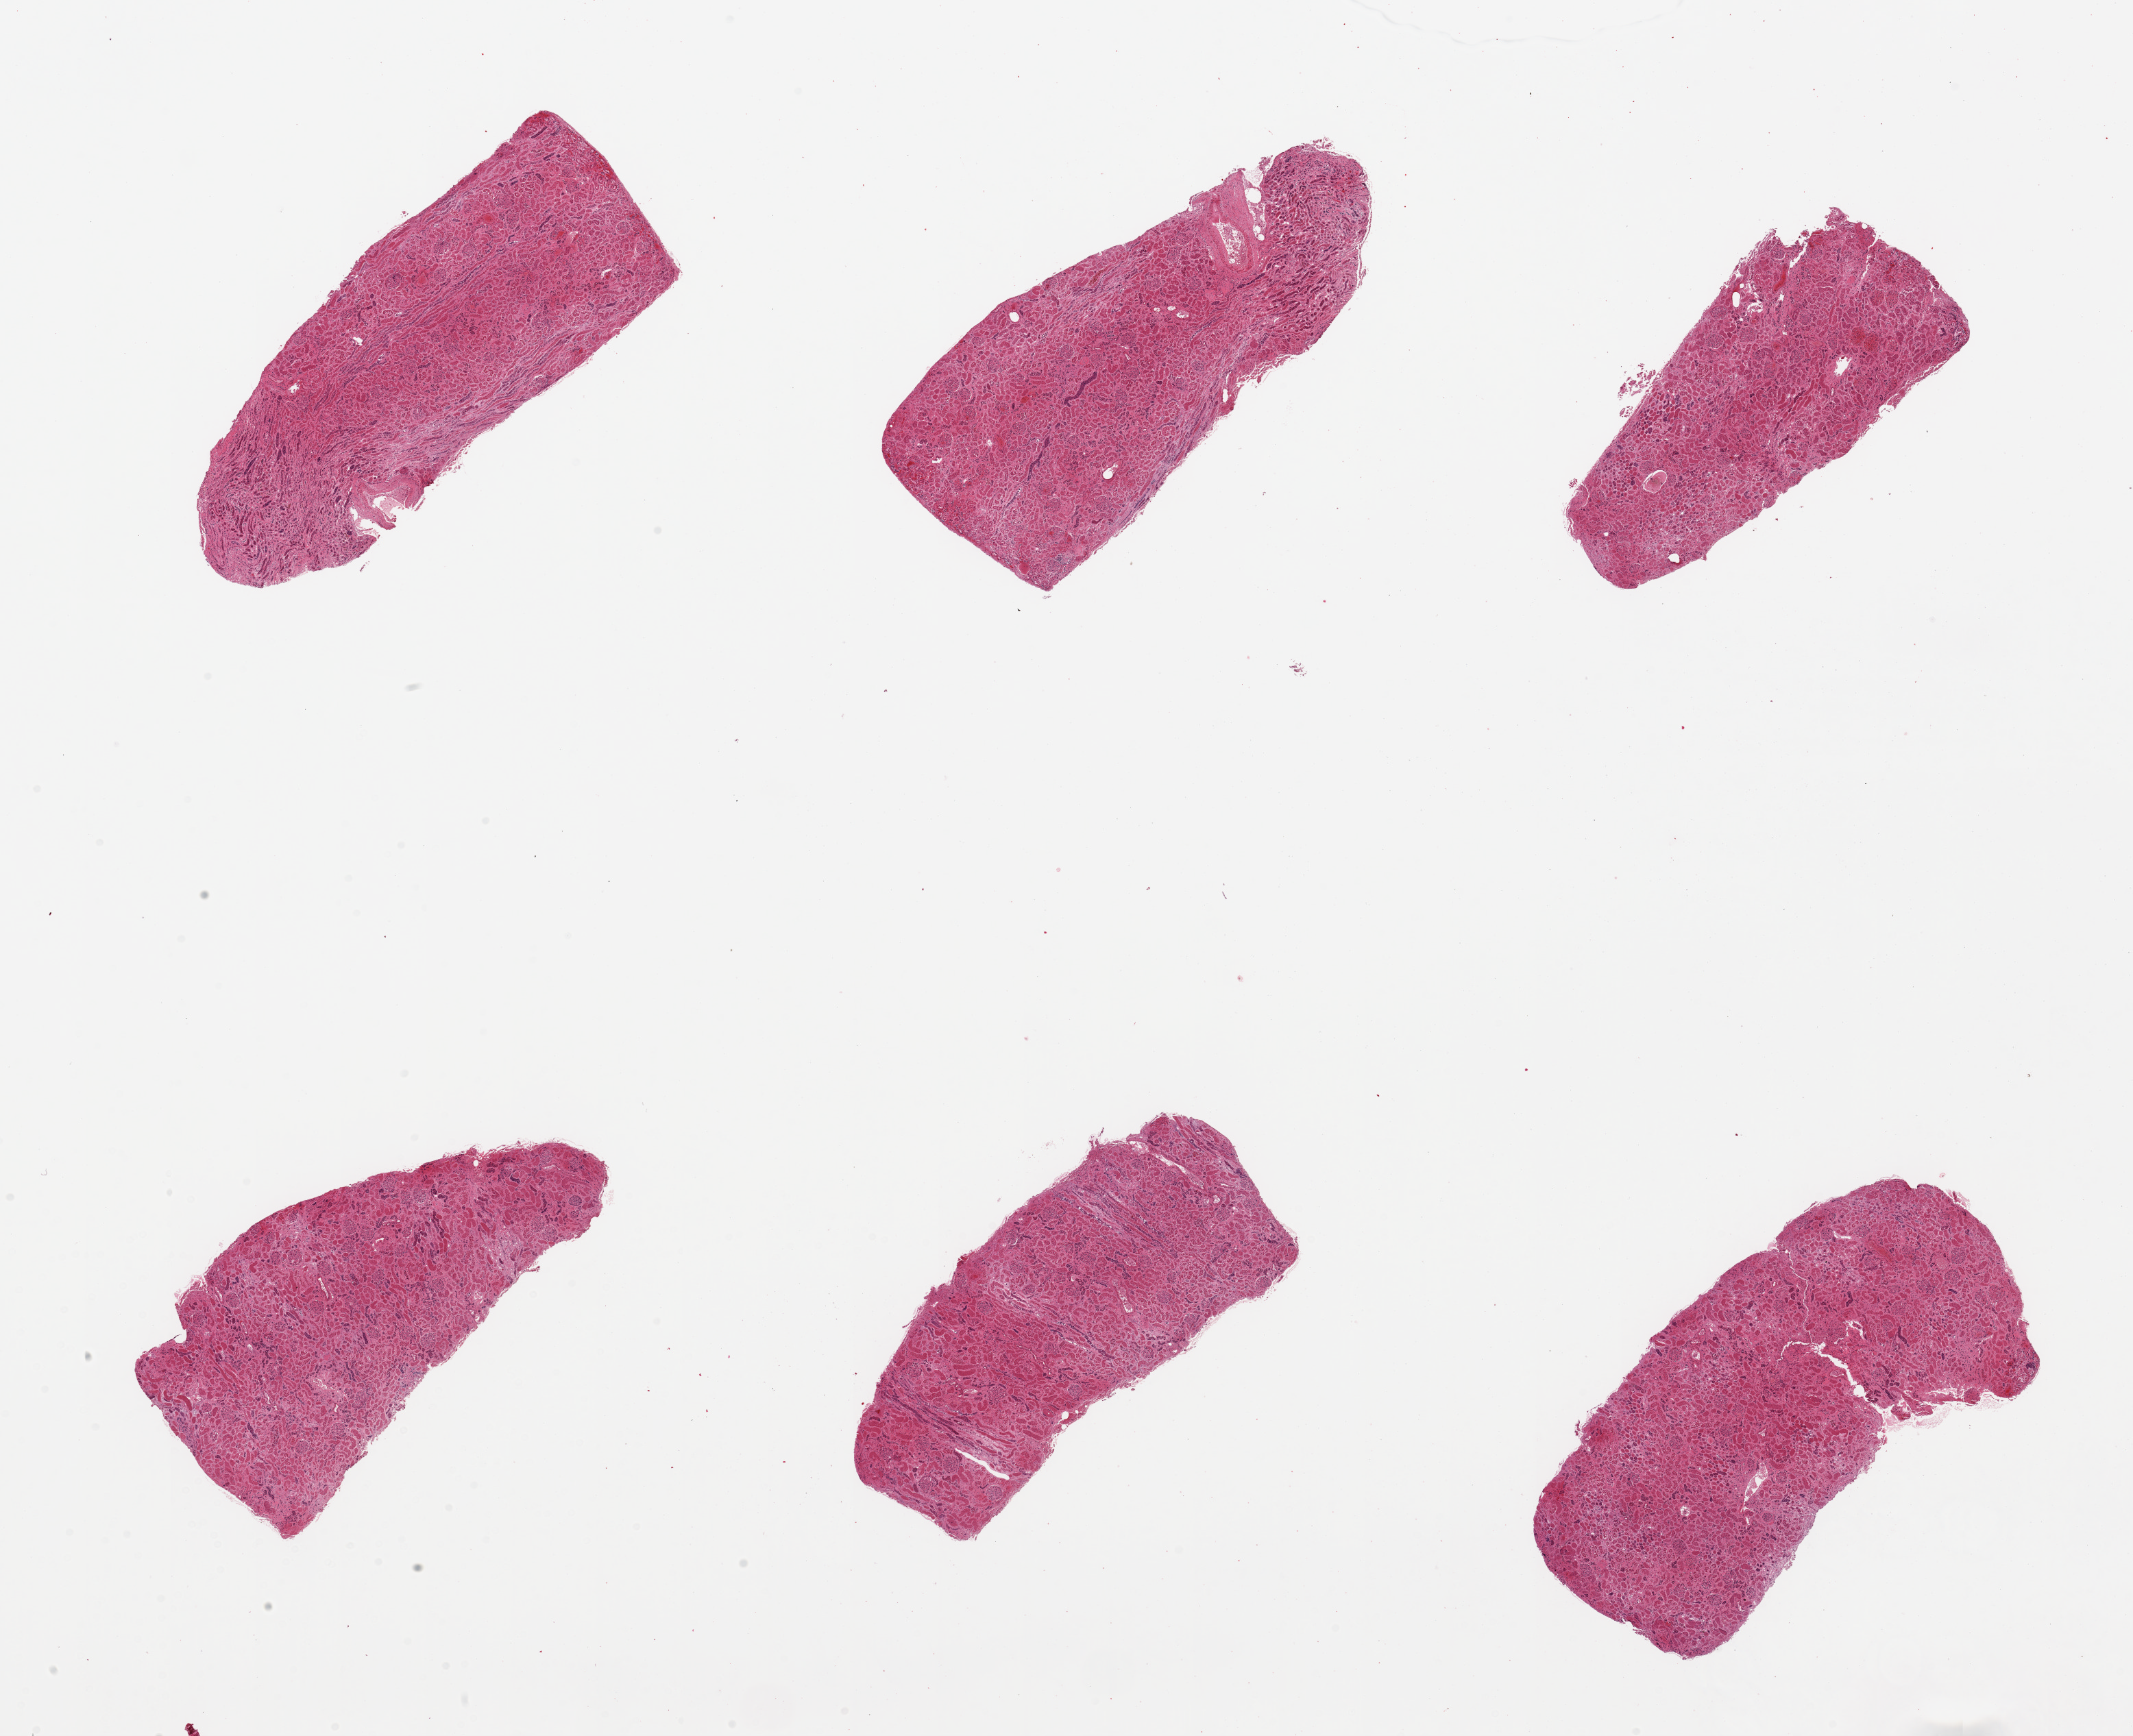
Haematoxylin and eosin whole-slide image, low-resolution overview of the scanned area, about 24.6 x 20.0 mm (slide scanned at 20x), PAXgene-fixed, paraffin-embedded tissue, section of renal cortex (target tissue), tissue donor sample.
Reviewer comment on this tissue sample: 6 pieces; tubules totally autolyzed.